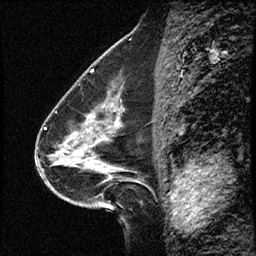
Breast MRI (dynamic contrast-enhanced), one sagittal slice. Slice 27 of 50 in the series (ordered by position). Dynamic contrast-enhanced study with each time point stored as its own series, time point 2 of 4 at this slice position (early post-contrast, ordered by acquisition time). 1.5 T. TE 4.2 ms, TR 17.5 ms. 3 mm slice thickness. 256 × 256 image matrix, field of view 200 × 200 mm. Case-level facts recorded for this patient, not image findings: setting: breast cancer imaged before/during neoadjuvant chemotherapy.
Structures marked on this image (semi-automatic segmentation, software-assisted and operator-edited):
- analysis volume of interest (the breast-tissue region the enhancement analysis was run in; not a lesion): bounding box [x1, y1, x2, y2] px = [52, 98, 158, 207]
- tumour enhancement mask (voxels above the 100 % enhancement threshold inside the analysis volume of interest): [102, 168, 107, 171]